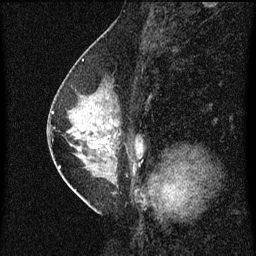
Breast MRI (dynamic contrast-enhanced), one sagittal slice. Slice 31 of 60 in the series (ordered by position). Dynamic contrast-enhanced series, image 2 of 3 at this slice position (ordered by acquisition). 1.5 T. TE 4.2 ms, TR 8 ms. 2 mm slice thickness. 256 × 256 image matrix, field of view 180 × 180 mm. Patient: female, 47 years.
Outlined on this slice (semi-automatic segmentation, software-assisted and operator-edited):
- analysis volume of interest (the breast-tissue region the enhancement analysis was run in; not a lesion): bounding box [x1, y1, x2, y2] px = [54, 80, 143, 187]
- tumour enhancement mask (voxels above the 70 % enhancement threshold inside the analysis volume of interest): [54, 112, 138, 173]